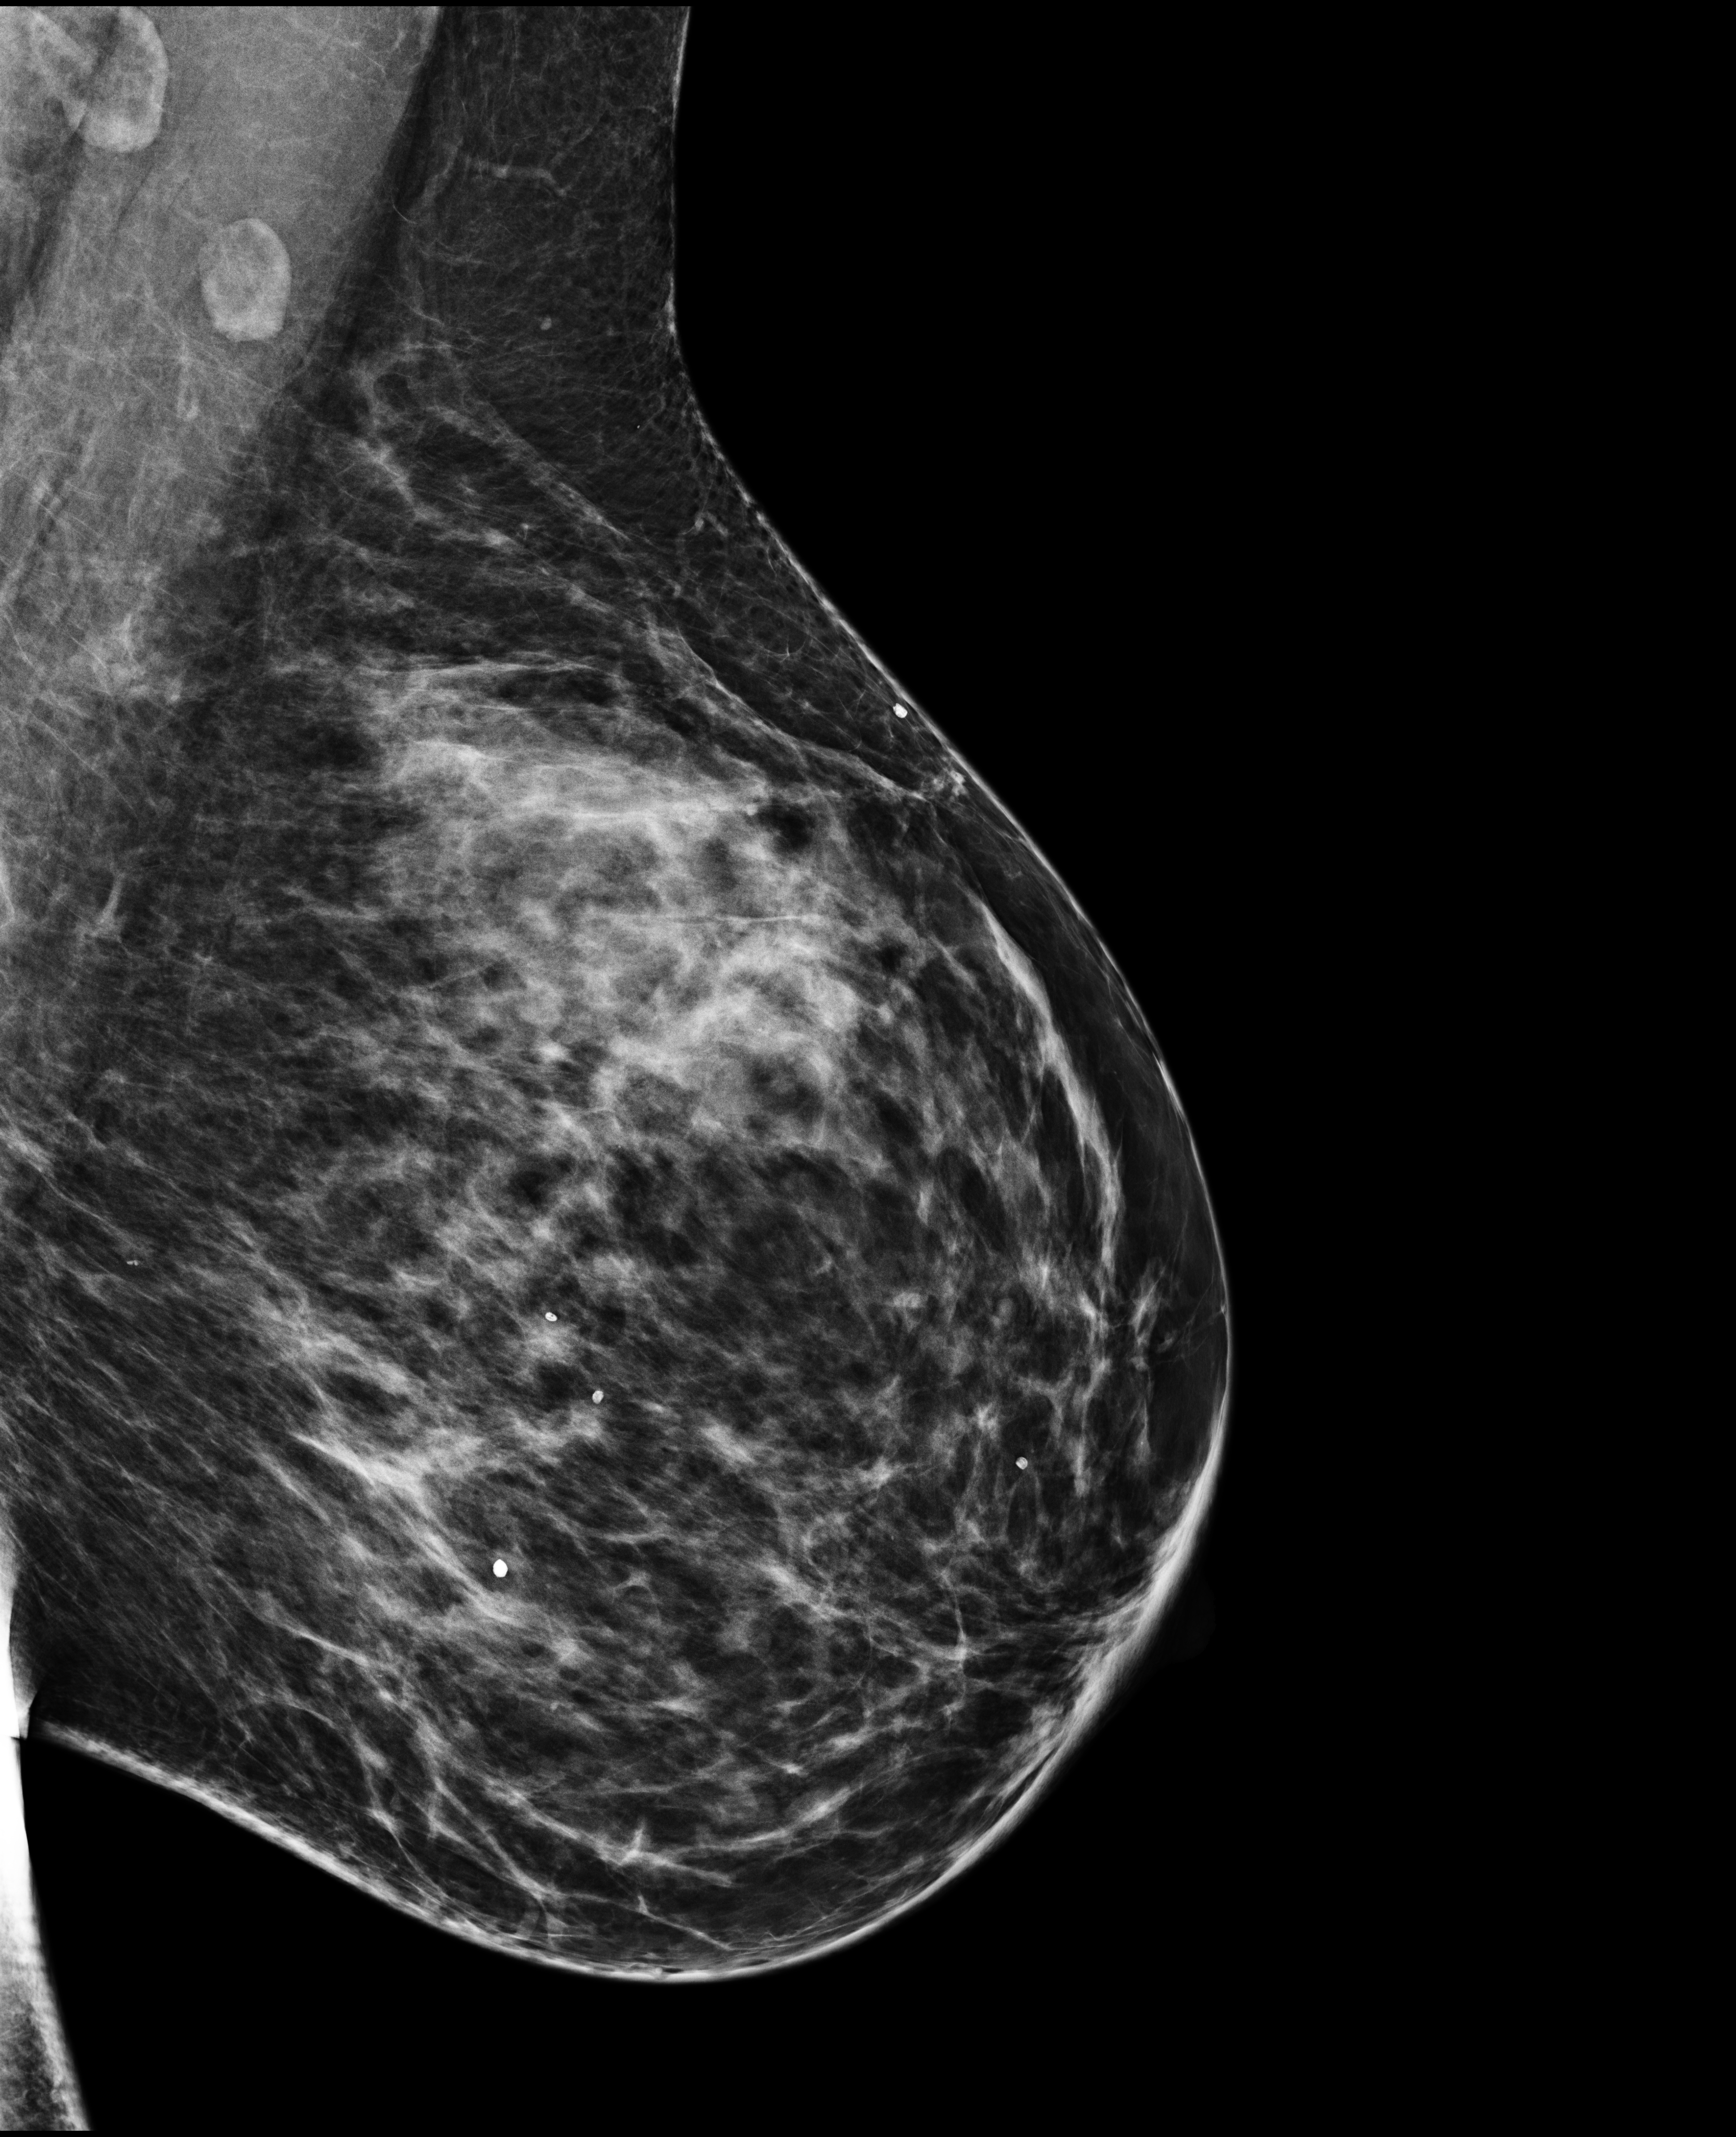
Annual screening mammography examination, system: Selenia Dimensions. Patient aged 44 years (female).
Image type: full-field digital mammogram. Breast: left. Projection: MLO view.